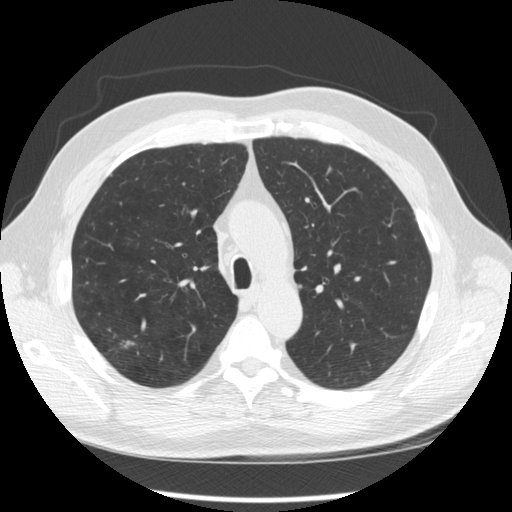
Low-dose screening chest CT, axial slice; second screening round (one year after baseline); lung window (W 1500 / L -600 HU); standard (soft-tissue) reconstruction kernel (STANDARD); 512 × 512 image matrix. Male participant, aged 64 years at enrolment. Former smoker at enrolment.
Expert reader's lesion annotation, bounding box (x1, y1, x2, y2) in pixels: (102, 327, 150, 369). The screening reader recorded 3 non-calcified nodules or masses ≥4 mm on this exam (right upper lobe, right upper lobe, right upper lobe); which of them this box marks is not recorded.